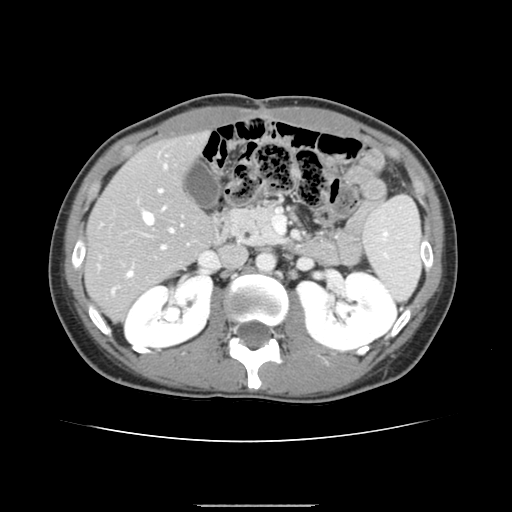
Contrast-enhanced abdominal CT, one axial slice; position 76 of 150 along the scan axis; 120 kVp; intravenous contrast given; soft-tissue window (W 400 / L 40 HU); 2.5 mm slice thickness; 512 × 512 image matrix. Female patient, age 32 years. Case-level facts recorded for this patient, not image findings: diagnosis: colorectal cancer liver metastases, imaged before liver resection; multiple liver metastases: yes; largest metastasis: 0.7 cm; chemotherapy before resection: yes.
Annotated regions visible in this slice (expert manual segmentation):
- hepatic veins: bounding box (x1, y1, x2, y2) in pixels: (127, 207, 173, 276)
- liver: (86, 134, 213, 318)
- planned liver remnant (the part of the liver to remain after resection): (87, 134, 212, 280)
- portal vein (with intrahepatic branches): (112, 164, 183, 294)